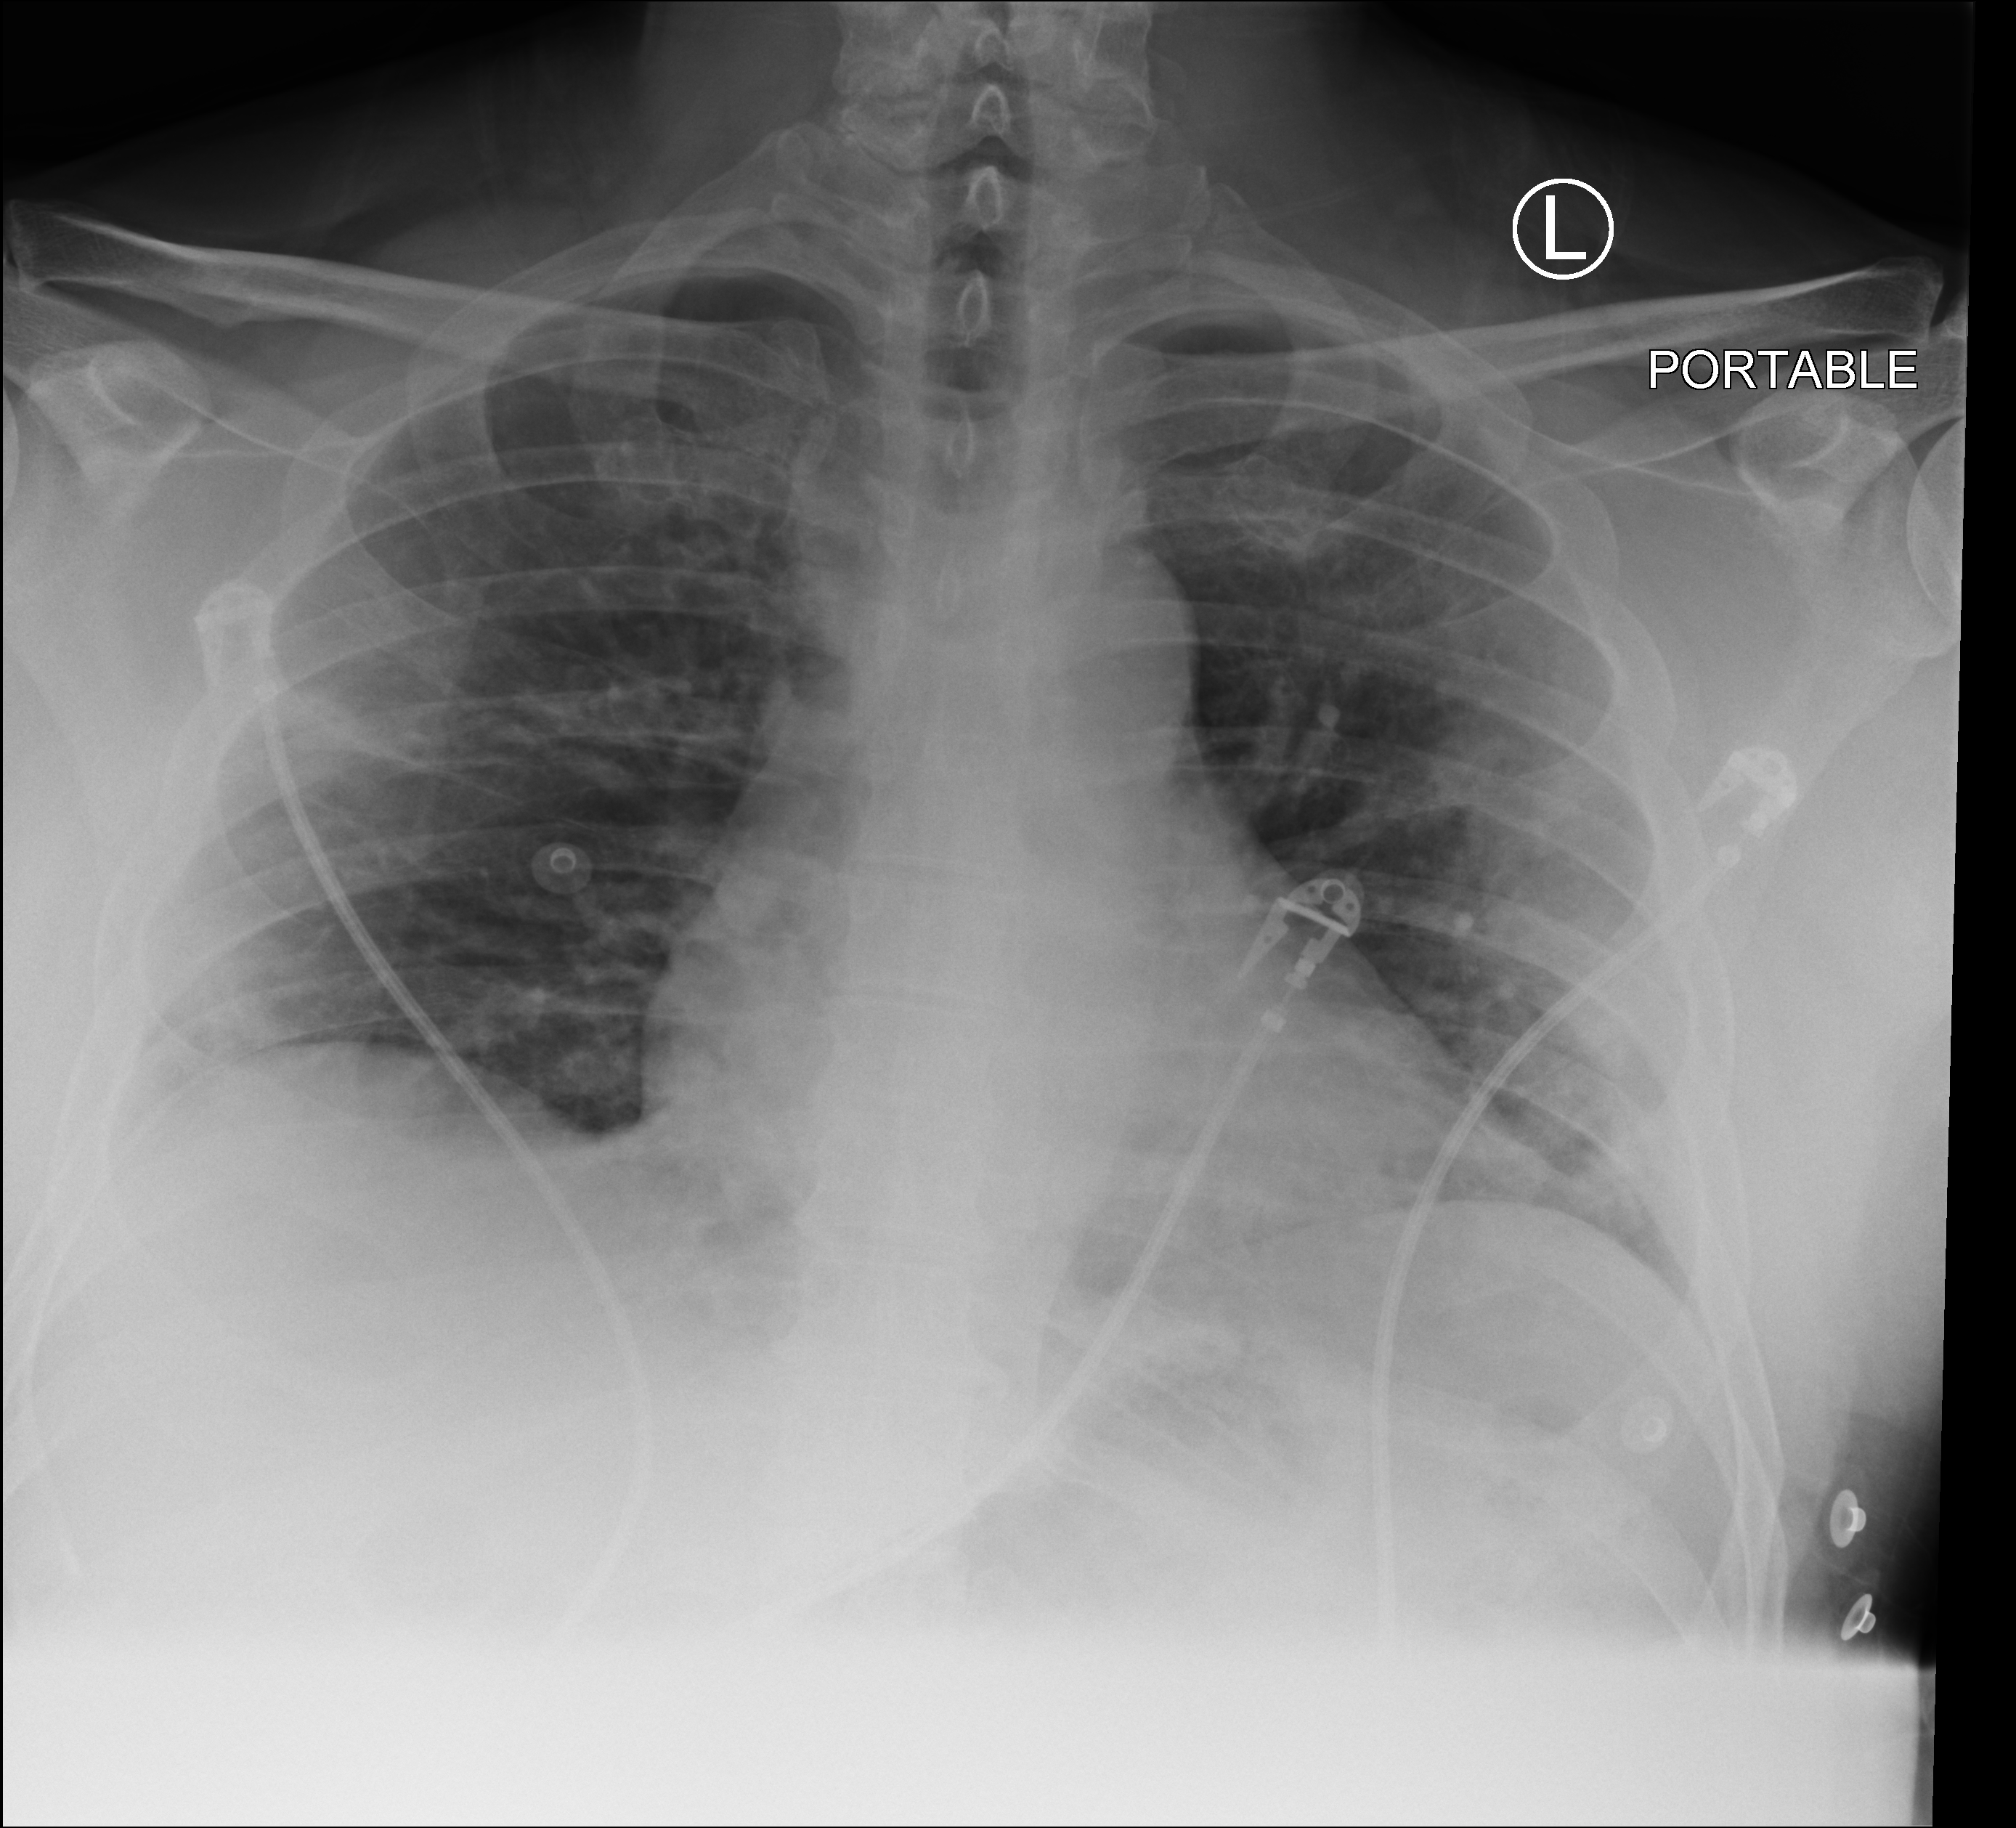
Portable chest radiograph; anteroposterior (AP) projection. Patient hospitalised with COVID-19; male, aged 18–59 years.
Hospital-stay facts (about this admission, not read from this image; timing relative to this image not recorded): length of hospital stay: 24 days; mechanically ventilated during this hospital stay: no; admitted to intensive care during this hospital stay: yes.